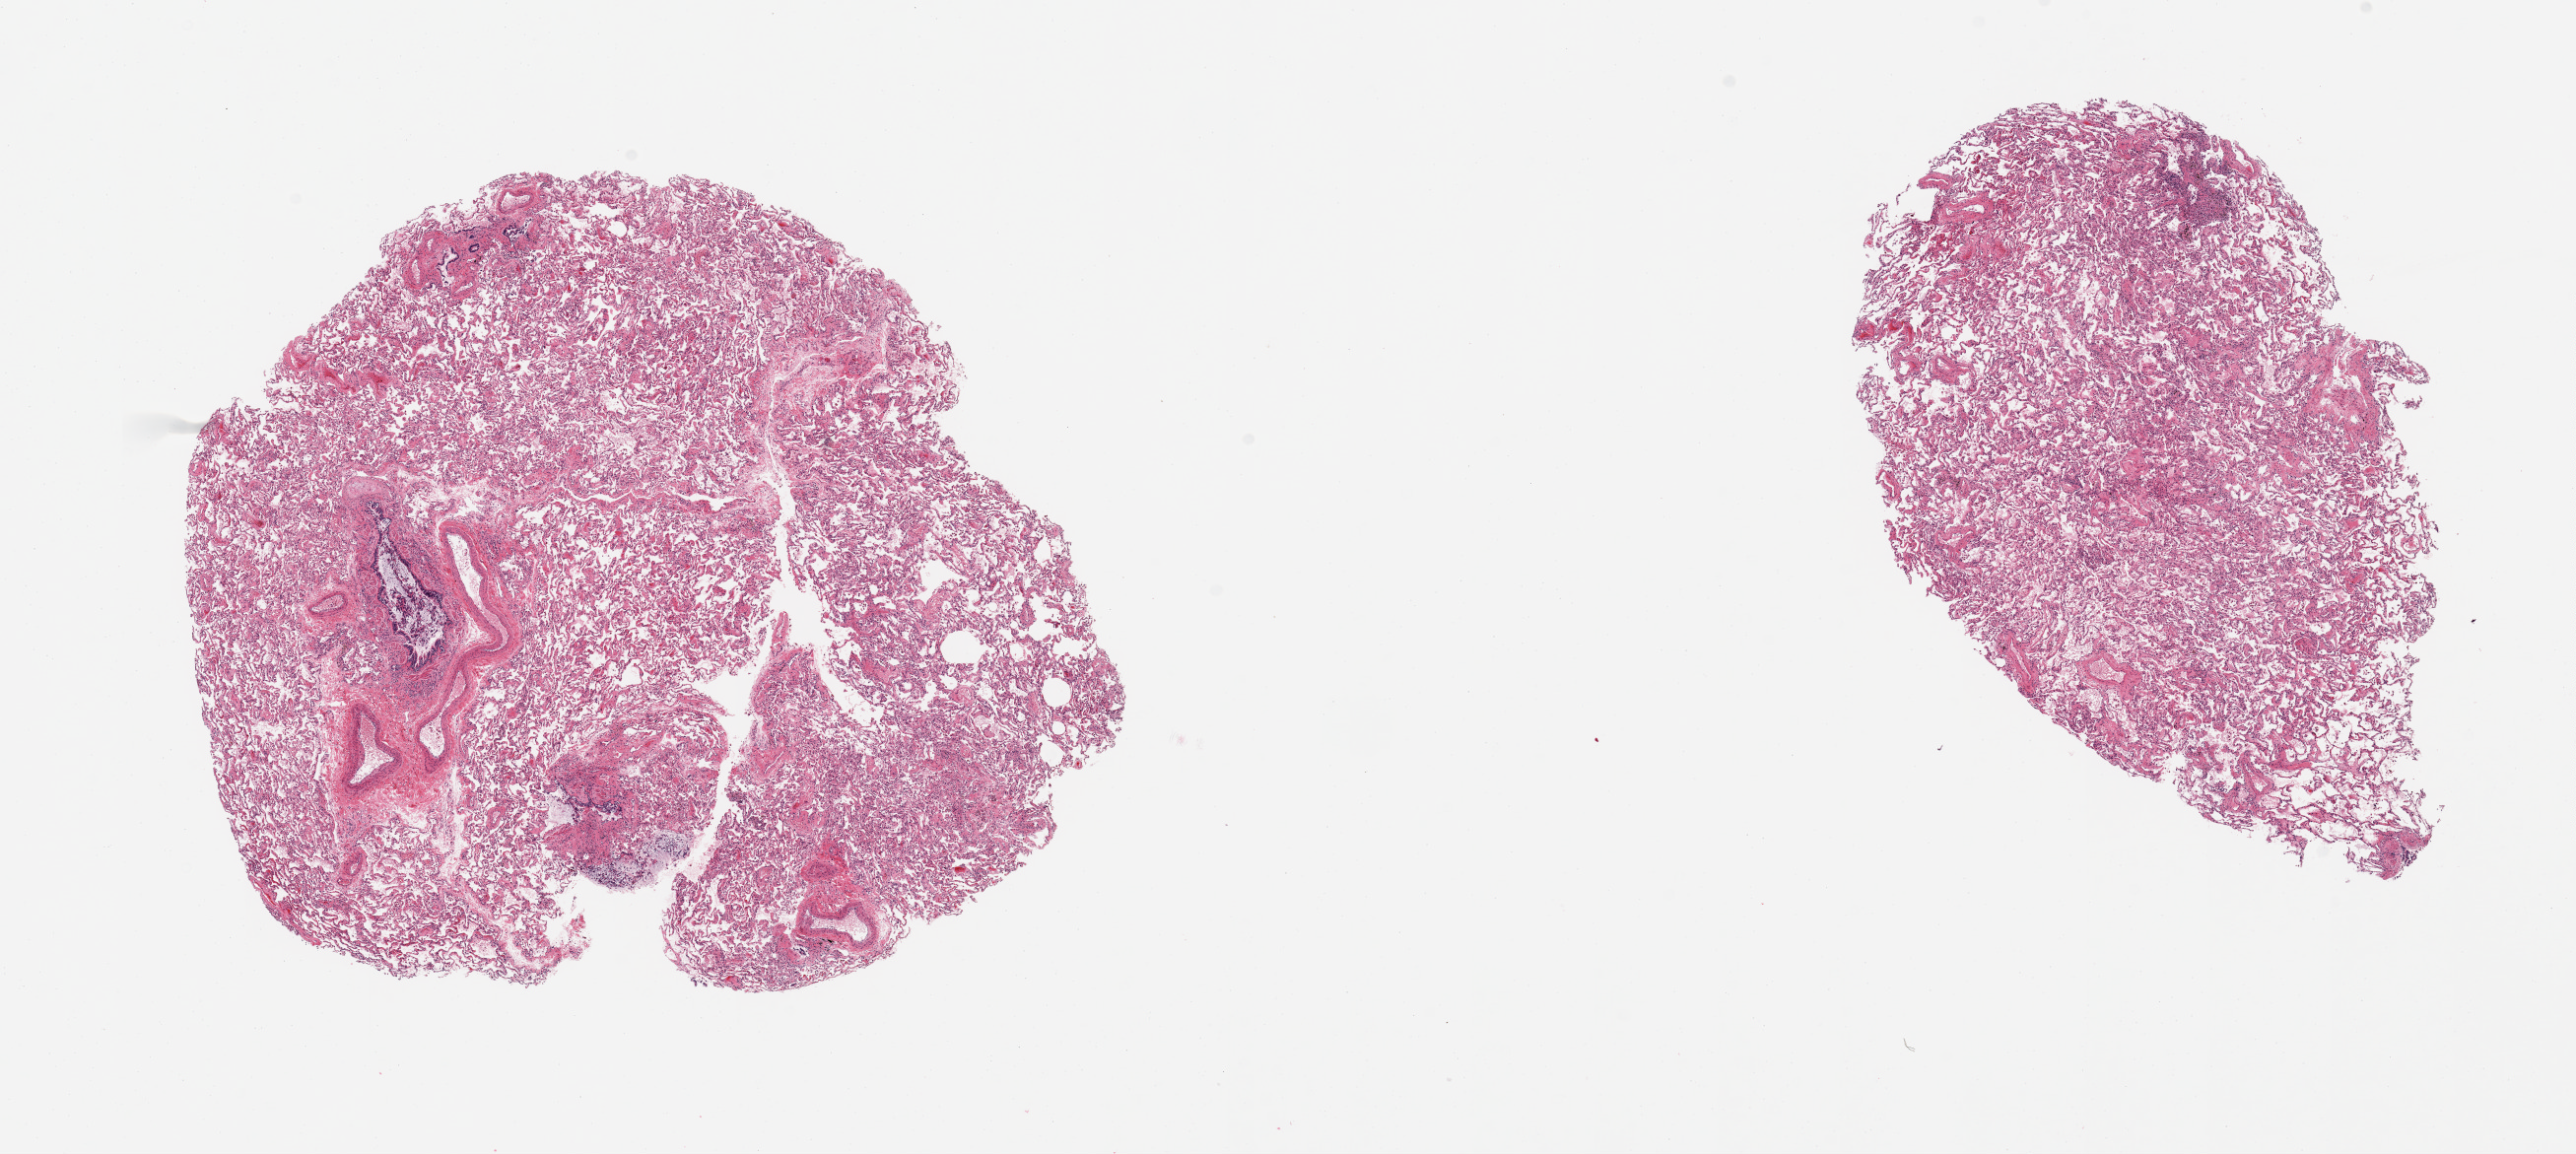
Hematoxylin and eosin (H&E) whole-slide image, brightfield, low-resolution overview of the scanned area, about 20.7 x 9.3 mm (slide scanned at 20x). PAXgene-fixed paraffin-embedded (PFPE) section. Target tissue: lung. Donor tissue sample. Donor: female.
Pathologist's review note for this sample: 2 pieces; some congestion and pigmented macrophages.